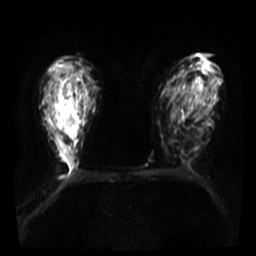
Breast MRI, one axial slice. Position 22 of 36 along the scan axis. Diffusion-weighted series; image 2 of 4 stored at this slice position (different b-values; order by instance number). 3 T. 256 × 256 image matrix. Female patient.
Outlined on this slice (outlined manually by an expert reader):
- tumour on diffusion-weighted imaging: bounding box [x1, y1, x2, y2] px = [65, 81, 74, 100]